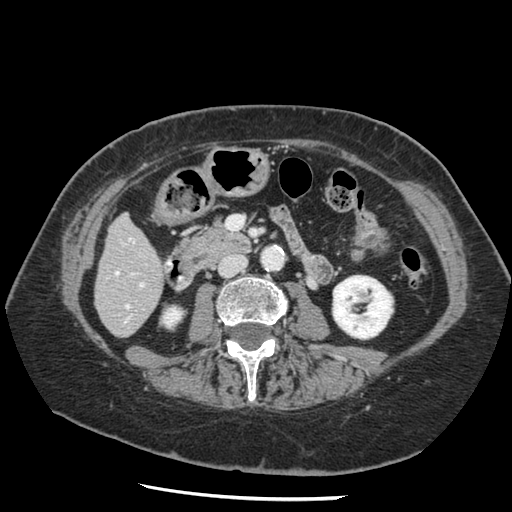
Contrast-enhanced abdominal CT, one axial slice; slice 40 of 148 in the series (ordered by position); reconstruction kernel STANDARD; 120 kVp; soft-tissue window (W 400 / L 40 HU); 2.5 mm slice thickness; 512 × 512 image matrix. Female patient, age 85 years. From the clinical record (not read from this slice): diagnosis: colorectal cancer liver metastases, imaged before liver resection; multiple liver metastases: no.
Annotated regions visible in this slice (outlined manually by an expert reader):
- hepatic veins: bounding box [x1, y1, x2, y2] px = [115, 271, 129, 308]
- liver: [96, 216, 164, 336]
- planned liver remnant (the part of the liver to remain after resection): [96, 216, 164, 334]